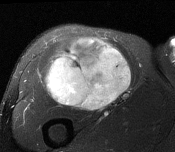
MRI of an extremity soft-tissue mass, one axial slice; position 98 of 116 along the scan axis; T2-weighted fat-saturated; MR volume resampled by the dataset authors to the PET/CT grid (not the native acquisition matrix); 3.27 mm slice thickness; 175 × 152 image matrix. Male patient. From the clinical record (not read from this slice): histological type: pleiomorphic leiomyosarcoma; grade: intermediate; site of the primary tumour: right thigh.
Annotated regions visible in this slice (expert contour drawn on MRI and transferred to this co-registered scan by the dataset authors):
- gross tumour volume including surrounding oedema: bounding box (x1, y1, x2, y2) in pixels: (45, 38, 132, 110)
- gross tumour volume (mass): (47, 38, 132, 110)